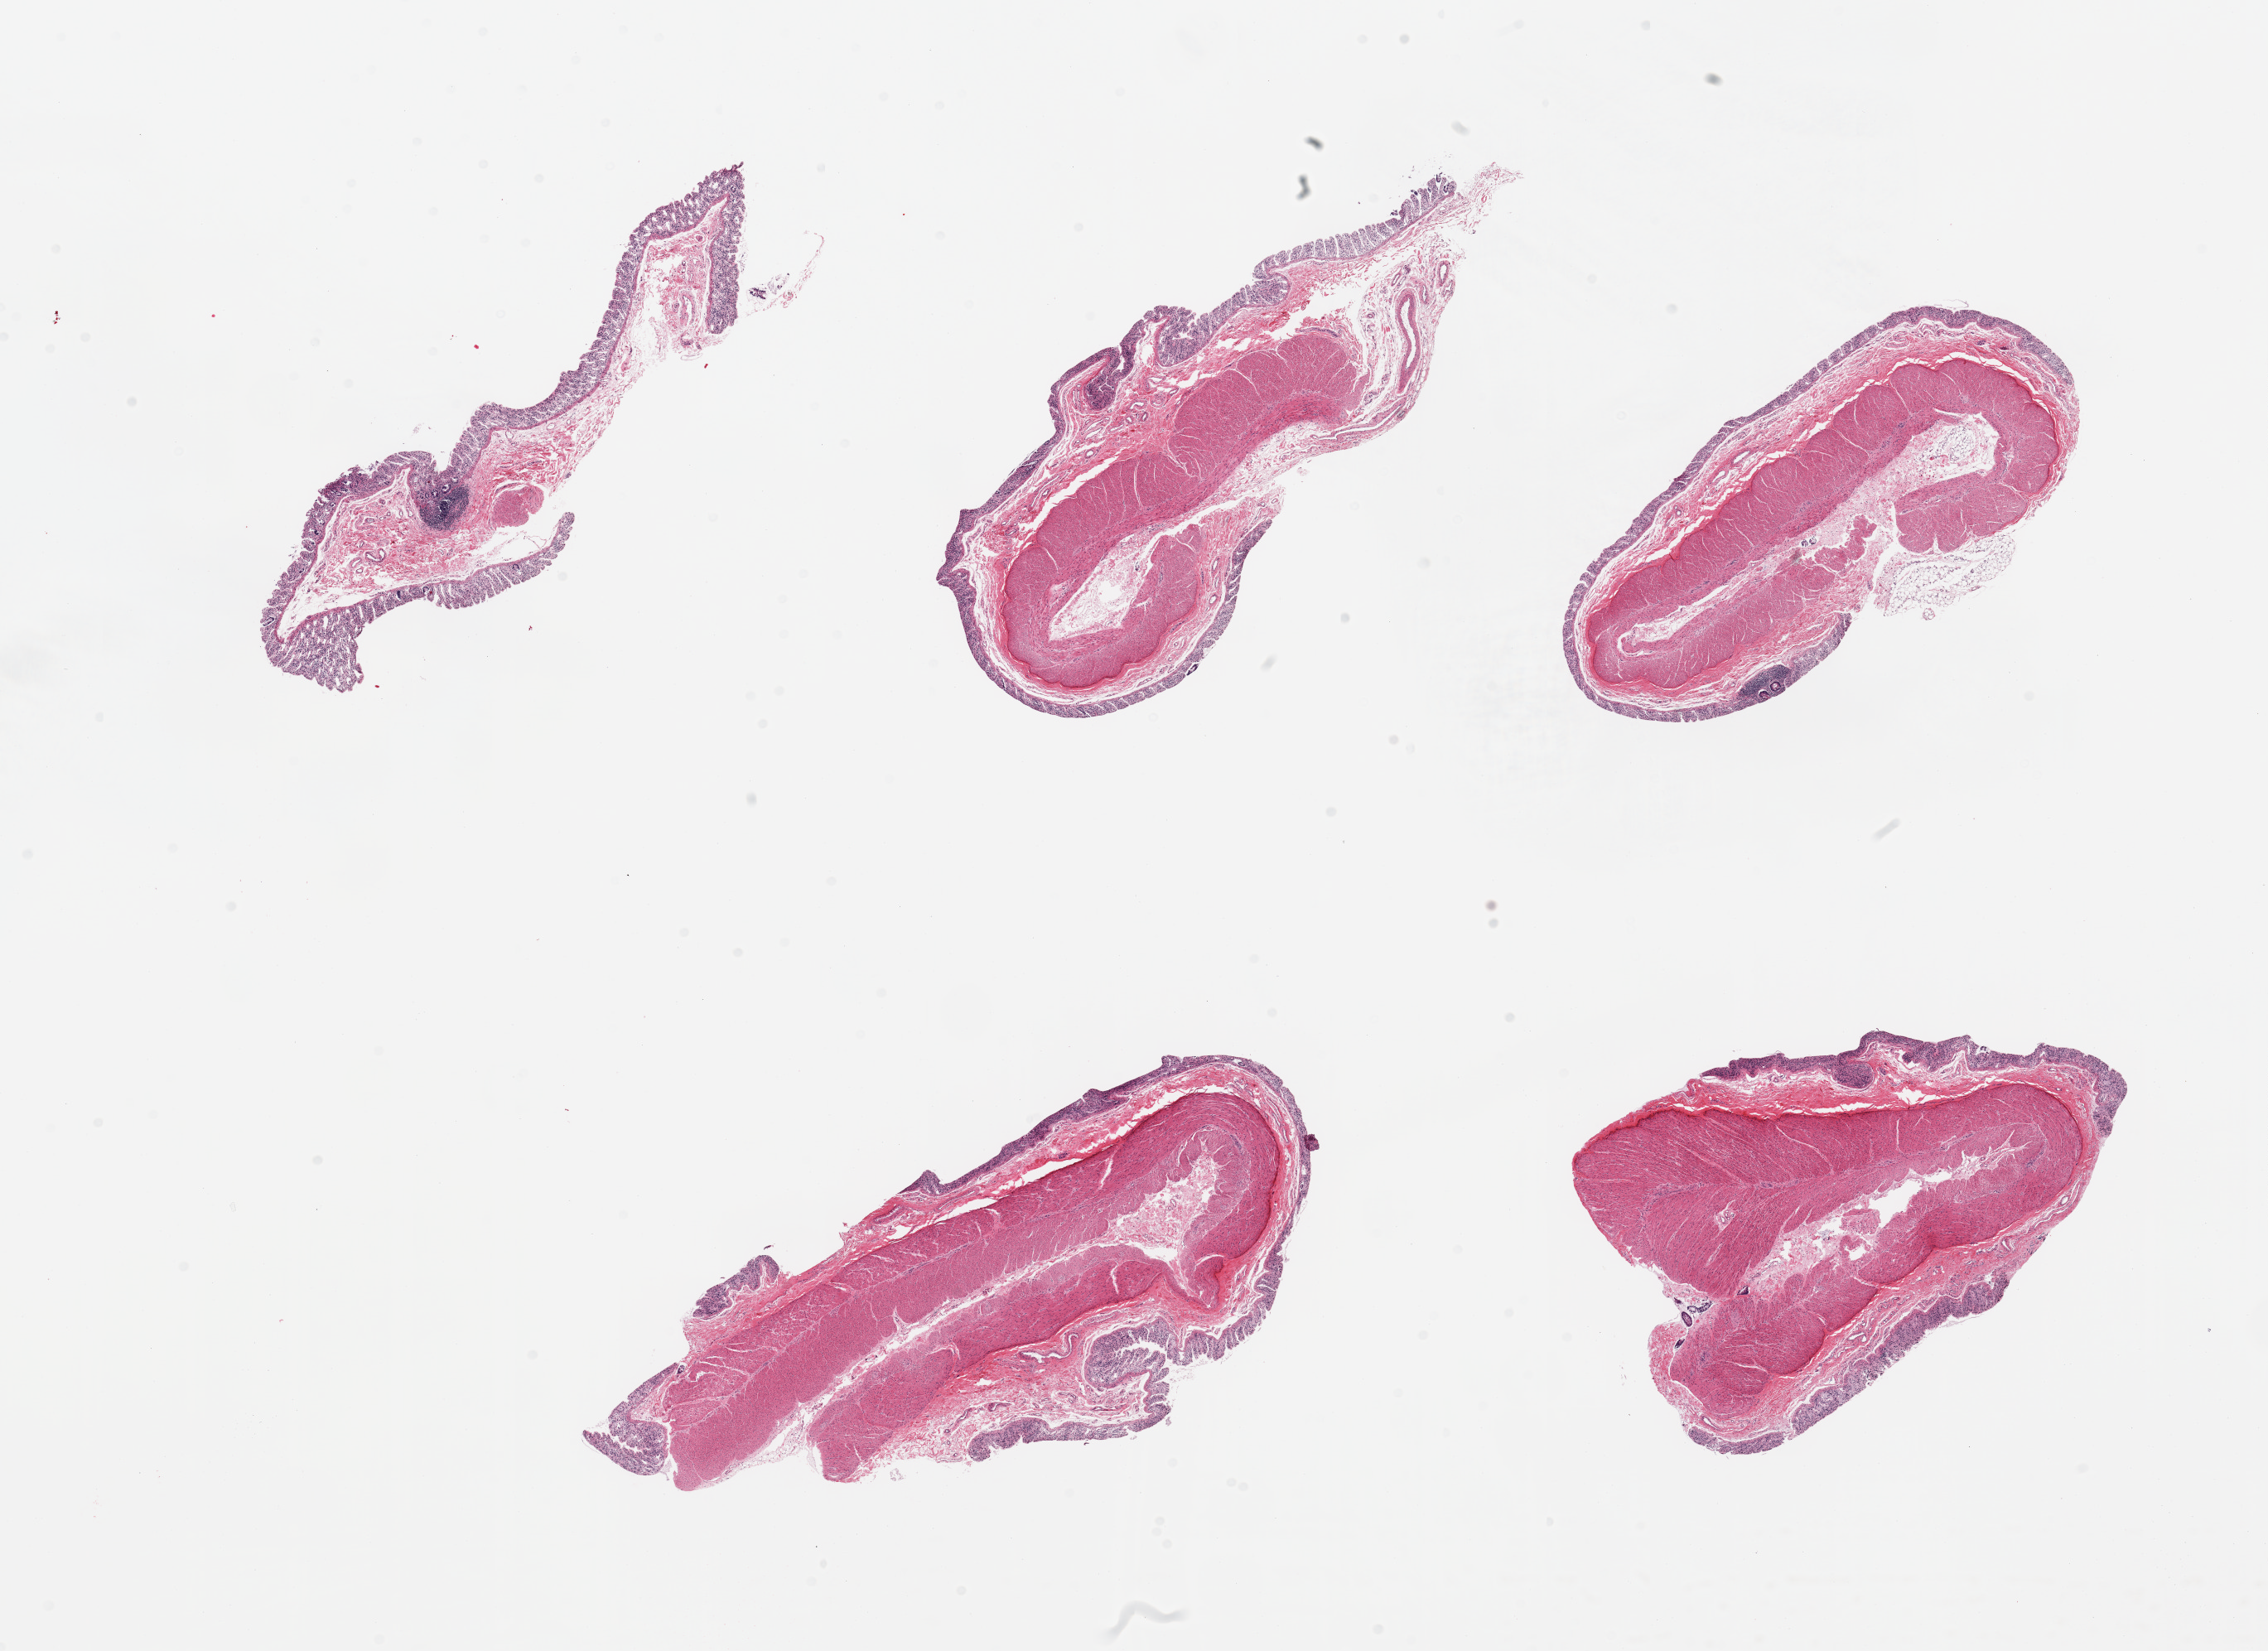
Digitized hematoxylin and eosin (H&E)-stained section — low-resolution overview of the scanned area, about 21.7 x 15.8 mm (slide scanned at 20x), PAXgene-fixed paraffin-embedded (PFPE) section, sampled site (target tissue): transverse colon, donor tissue sample. Male donor.
Reviewer comment on this tissue sample: 6 pieces; mucosa autolyzed, muscle intact; 1 piece has no muscularis.